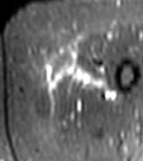
MRI of an extremity soft-tissue mass, one axial slice; slice 12 of 81 in the series (ordered by position); STIR; MR volume resampled by the dataset authors to the PET/CT grid (not the native acquisition matrix); 143 × 161 image matrix, field of view 140 × 157 mm. Female patient. From the clinical record (not read from this slice): histological type: myxofibrosarcoma; grade: intermediate; site of the primary tumour: left thigh.
Annotated regions visible in this slice (expert contour drawn on MRI and transferred to this co-registered scan by the dataset authors):
- gross tumour volume including surrounding oedema: bounding box (x1, y1, x2, y2) in pixels: (38, 58, 112, 98)